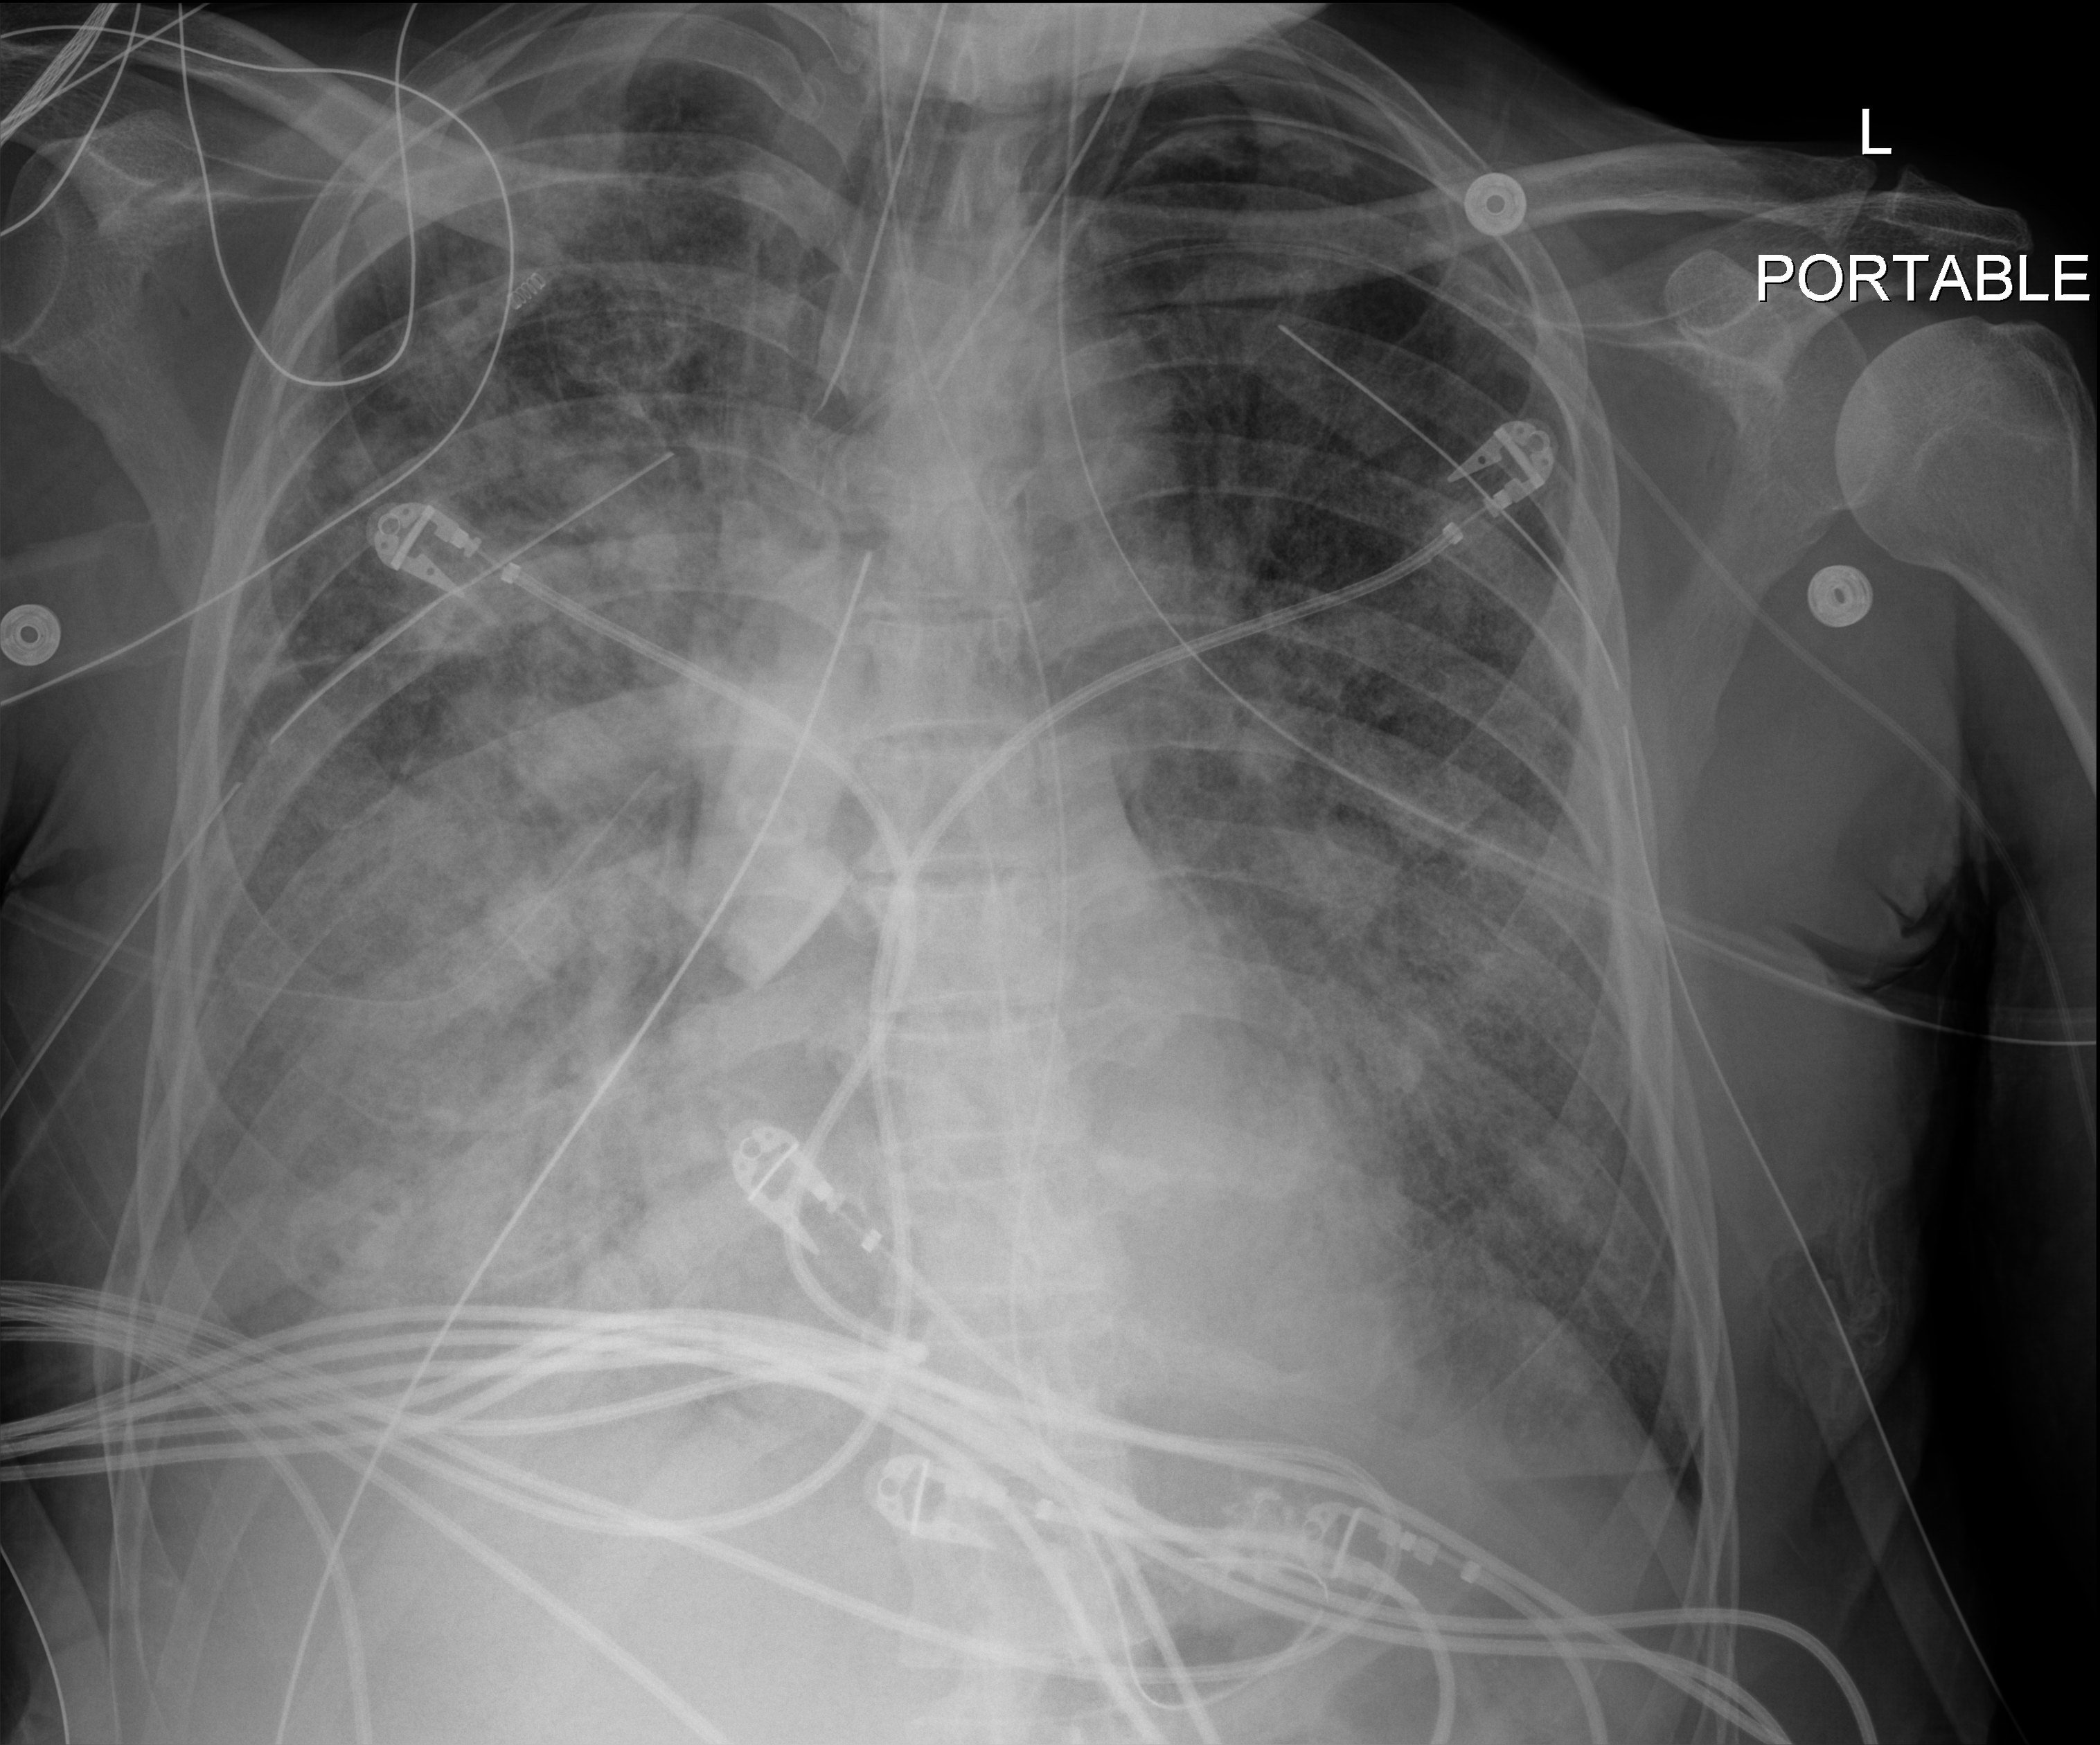
Portable chest radiograph; anteroposterior (AP) projection. Patient hospitalised with COVID-19; male, aged 60–74 years.
Admission-level facts for this patient (not findings on this image; timing relative to this image not recorded): admitted to intensive care during this hospital stay: yes; mechanically ventilated during this hospital stay: yes.